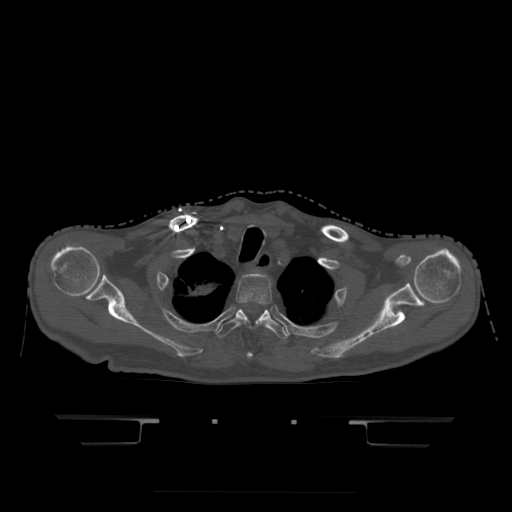
CT including the spine, one axial slice; position 379 of 522 along the scan axis; bone window (W 1800 / L 400 HU); 1.25 mm slice thickness; 512 × 512 image matrix. Patient age 68 years. Case-level facts recorded for this patient, not image findings: primary cancer: urothelial.
Annotated regions visible in this slice (semi-automatically segmented with operator editing):
- T2 vertebra: box from (x=236, y=274) to (x=272, y=358) px
- T3 vertebra: (x=216, y=309)–(x=288, y=340)